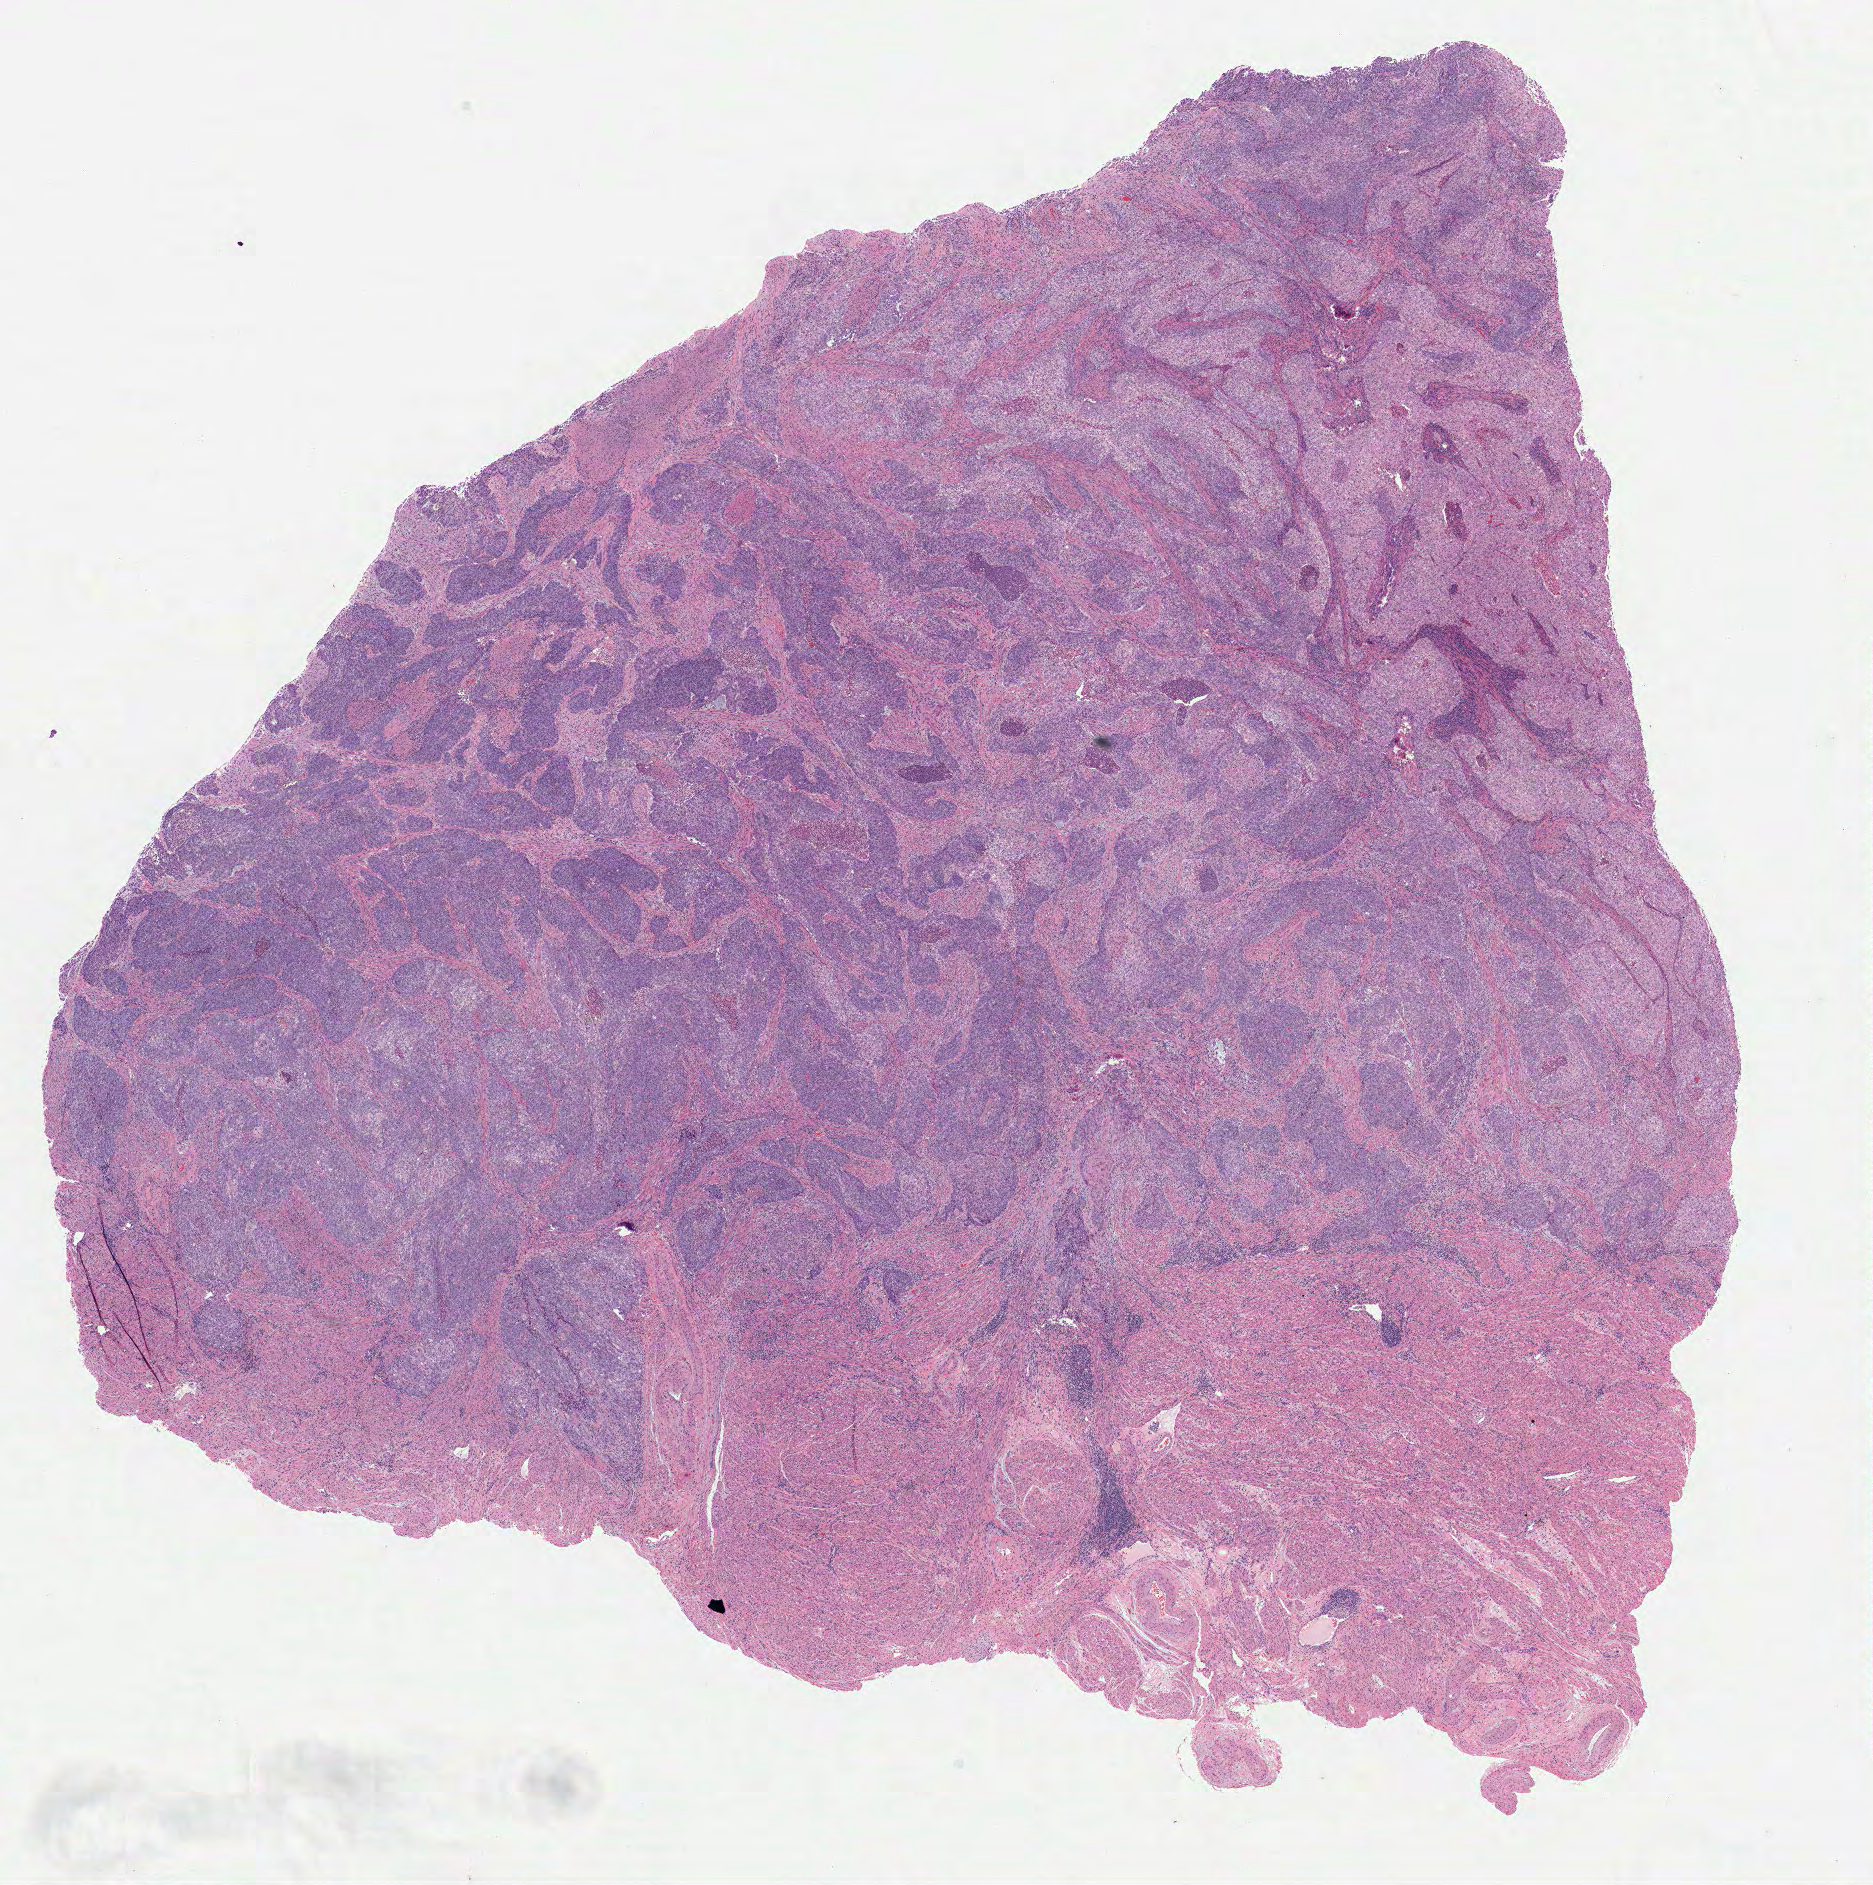
Digitized H&E tissue section (whole slide) — a low-resolution overview of the entire scanned area, about 15.0 x 15.1 mm (slide scanned at 20x), FFPE section, sample: primary tumour, uterus. Patient: female, age at initial diagnosis 87 years. Histologic grade: G3 (poorly differentiated).
Pathologic diagnosis: Endometrioid adenocarcinoma, NOS (endometrium). FIGO stage: IB.